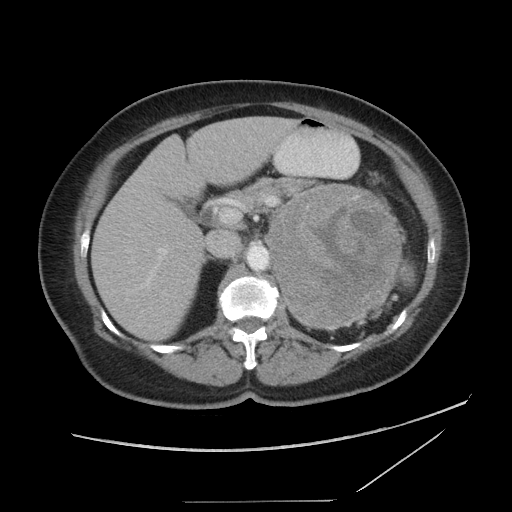
Contrast-enhanced abdominal CT, one axial slice; position 57 of 86 along the scan axis; reconstruction kernel STANDARD; intravenous contrast given; soft-tissue window (W 400 / L 40 HU); 5 mm slice thickness; 512 × 512 image matrix, field of view 398 × 398 mm. Female patient, age 77 years. From the clinical record (not read from this slice): diagnosis: adrenocortical carcinoma; tumour side: left adrenal; tumour size at pathology: 13.1 cm; Ki-67 index: 10 %; stage (as recorded): 3.
Structures marked on this image (semi-automatic segmentation, software-assisted and operator-edited):
- mass: bounding box [x1, y1, x2, y2] px = [267, 186, 401, 327]